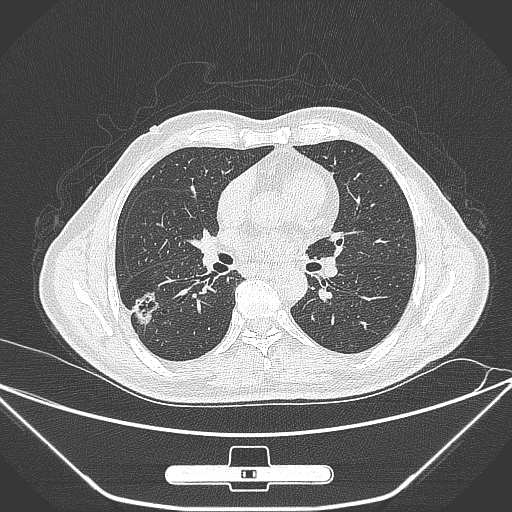
Chest CT, one axial slice. Slice 147 of 309 in the series (ordered by position). Lung window (W 1500 / L -600 HU). 1 mm slice thickness. 512 × 512 image matrix, field of view 398 × 398 mm. Male patient, age 71 years. From the clinical record (not read from this slice): clinical TNM (as recorded): T1c N0 M0.
Structures marked on this image (rectangle marked by the reading radiologist):
- lung tumour (recorded histology: adenocarcinoma): bounding box <127,285,164,331> (left, top, right, bottom; pixels)